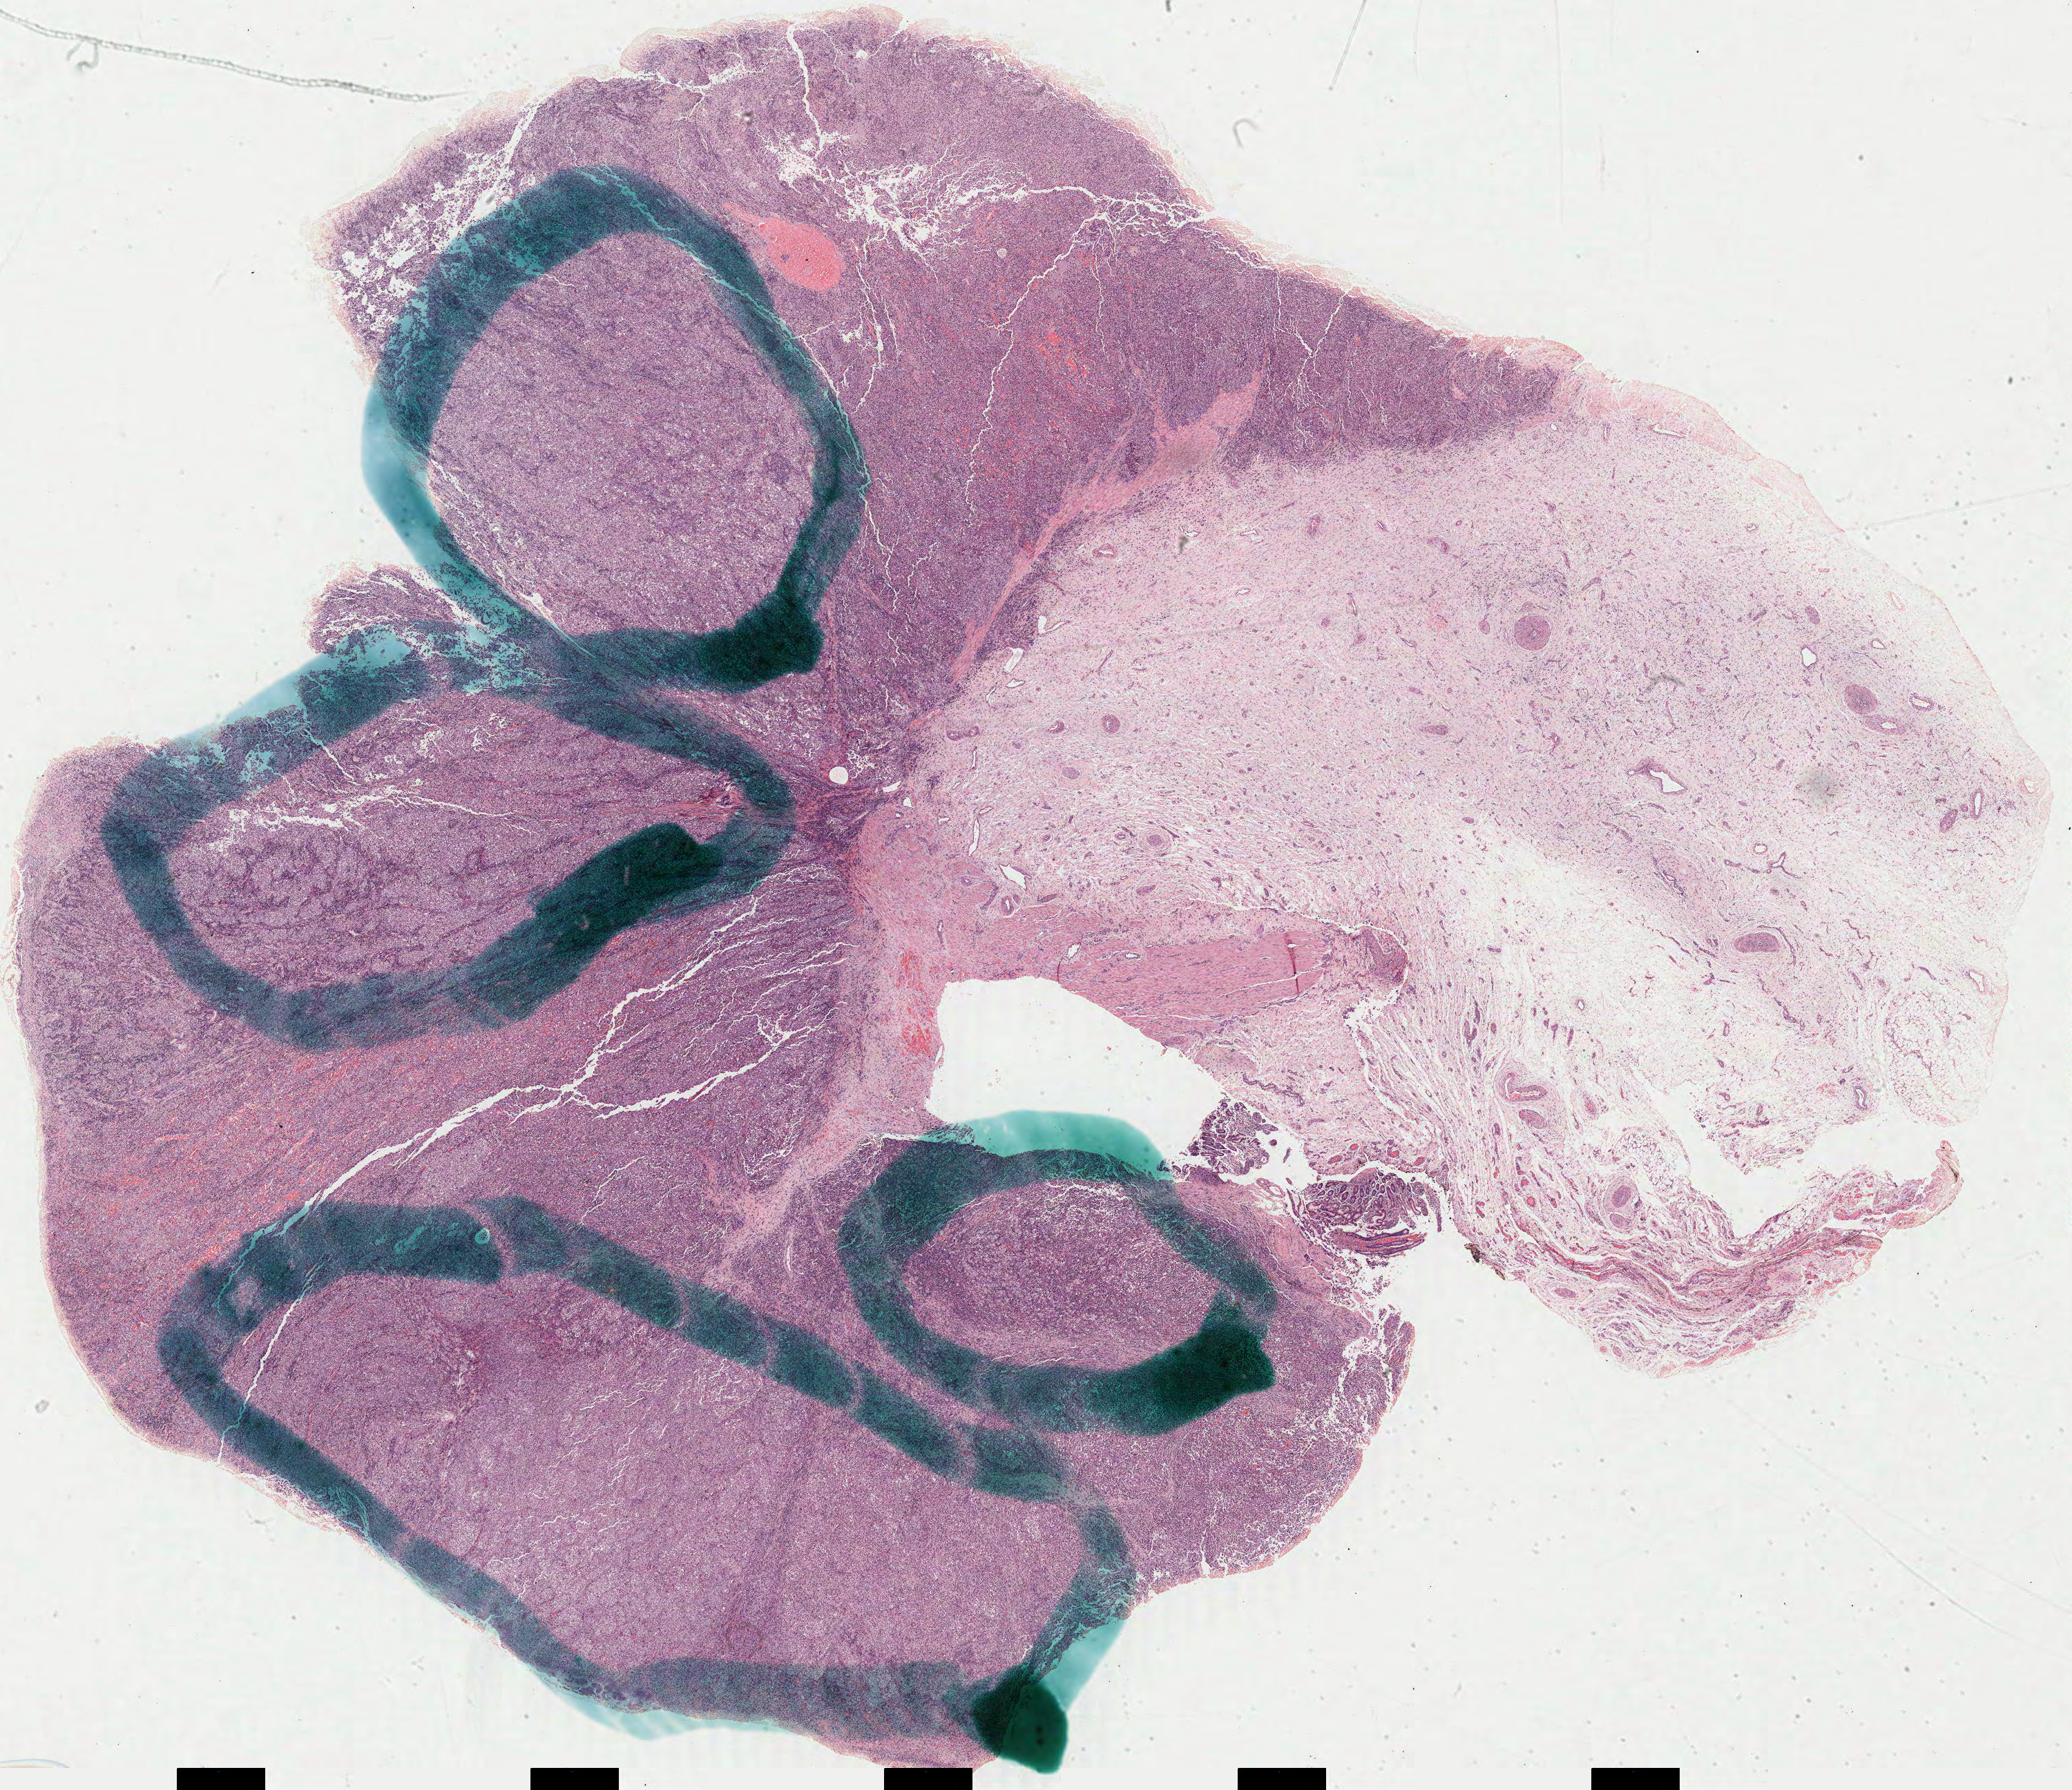
Whole-slide histology image, Hematoxylin and eosin (H&E) stained, low-resolution overview of the scanned area, about 24.1 x 20.8 mm (from a 40x scan). Formalin-fixed paraffin-embedded (FFPE) diagnostic section. Metastatic tumour sample, sampled site not recorded. Patient: female, age at initial diagnosis 27 years.
This section: metastatic tumour tissue. Patient diagnosis: Malignant melanoma, NOS.